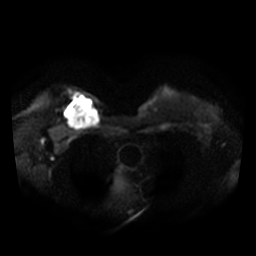
Breast MRI, one axial slice. Slice 29 of 36 in the series (ordered by position). Diffusion-weighted series; image 2 of 4 stored at this slice position (different b-values; order by instance number). 3 T. 5 mm slice thickness. 256 × 256 image matrix, field of view 340 × 340 mm. Female patient.
Annotated regions visible in this slice (manually delineated by an expert):
- tumour on diffusion-weighted imaging: box from (x=64, y=98) to (x=98, y=130) px